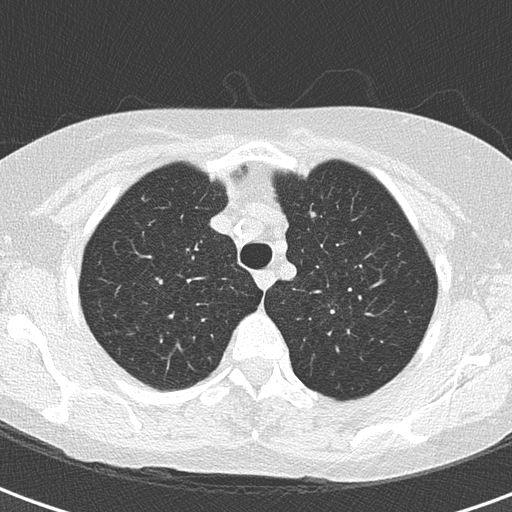
Chest CT (low-dose screening protocol), one axial image; baseline screening round; lung window (W 1500 / L -600 HU); 2 mm slice thickness. Female participant, aged 64 years at enrolment. Current smoker at enrolment.
• Expert-annotated lung lesion, box from (x=293, y=201) to (x=331, y=238) px.
• No non-calcified nodule or mass ≥4 mm was recorded by the screening reader at this exam.
• Official screen result: negative screen, minor abnormalities not suspicious for lung cancer.
• Lung cancer was diagnosed 508 days after this screen (after the second annual screen): adenocarcinoma, NOS, left upper lobe, moderately differentiated (G2), stage IA (AJCC 6th edition), 7 mm at pathology.